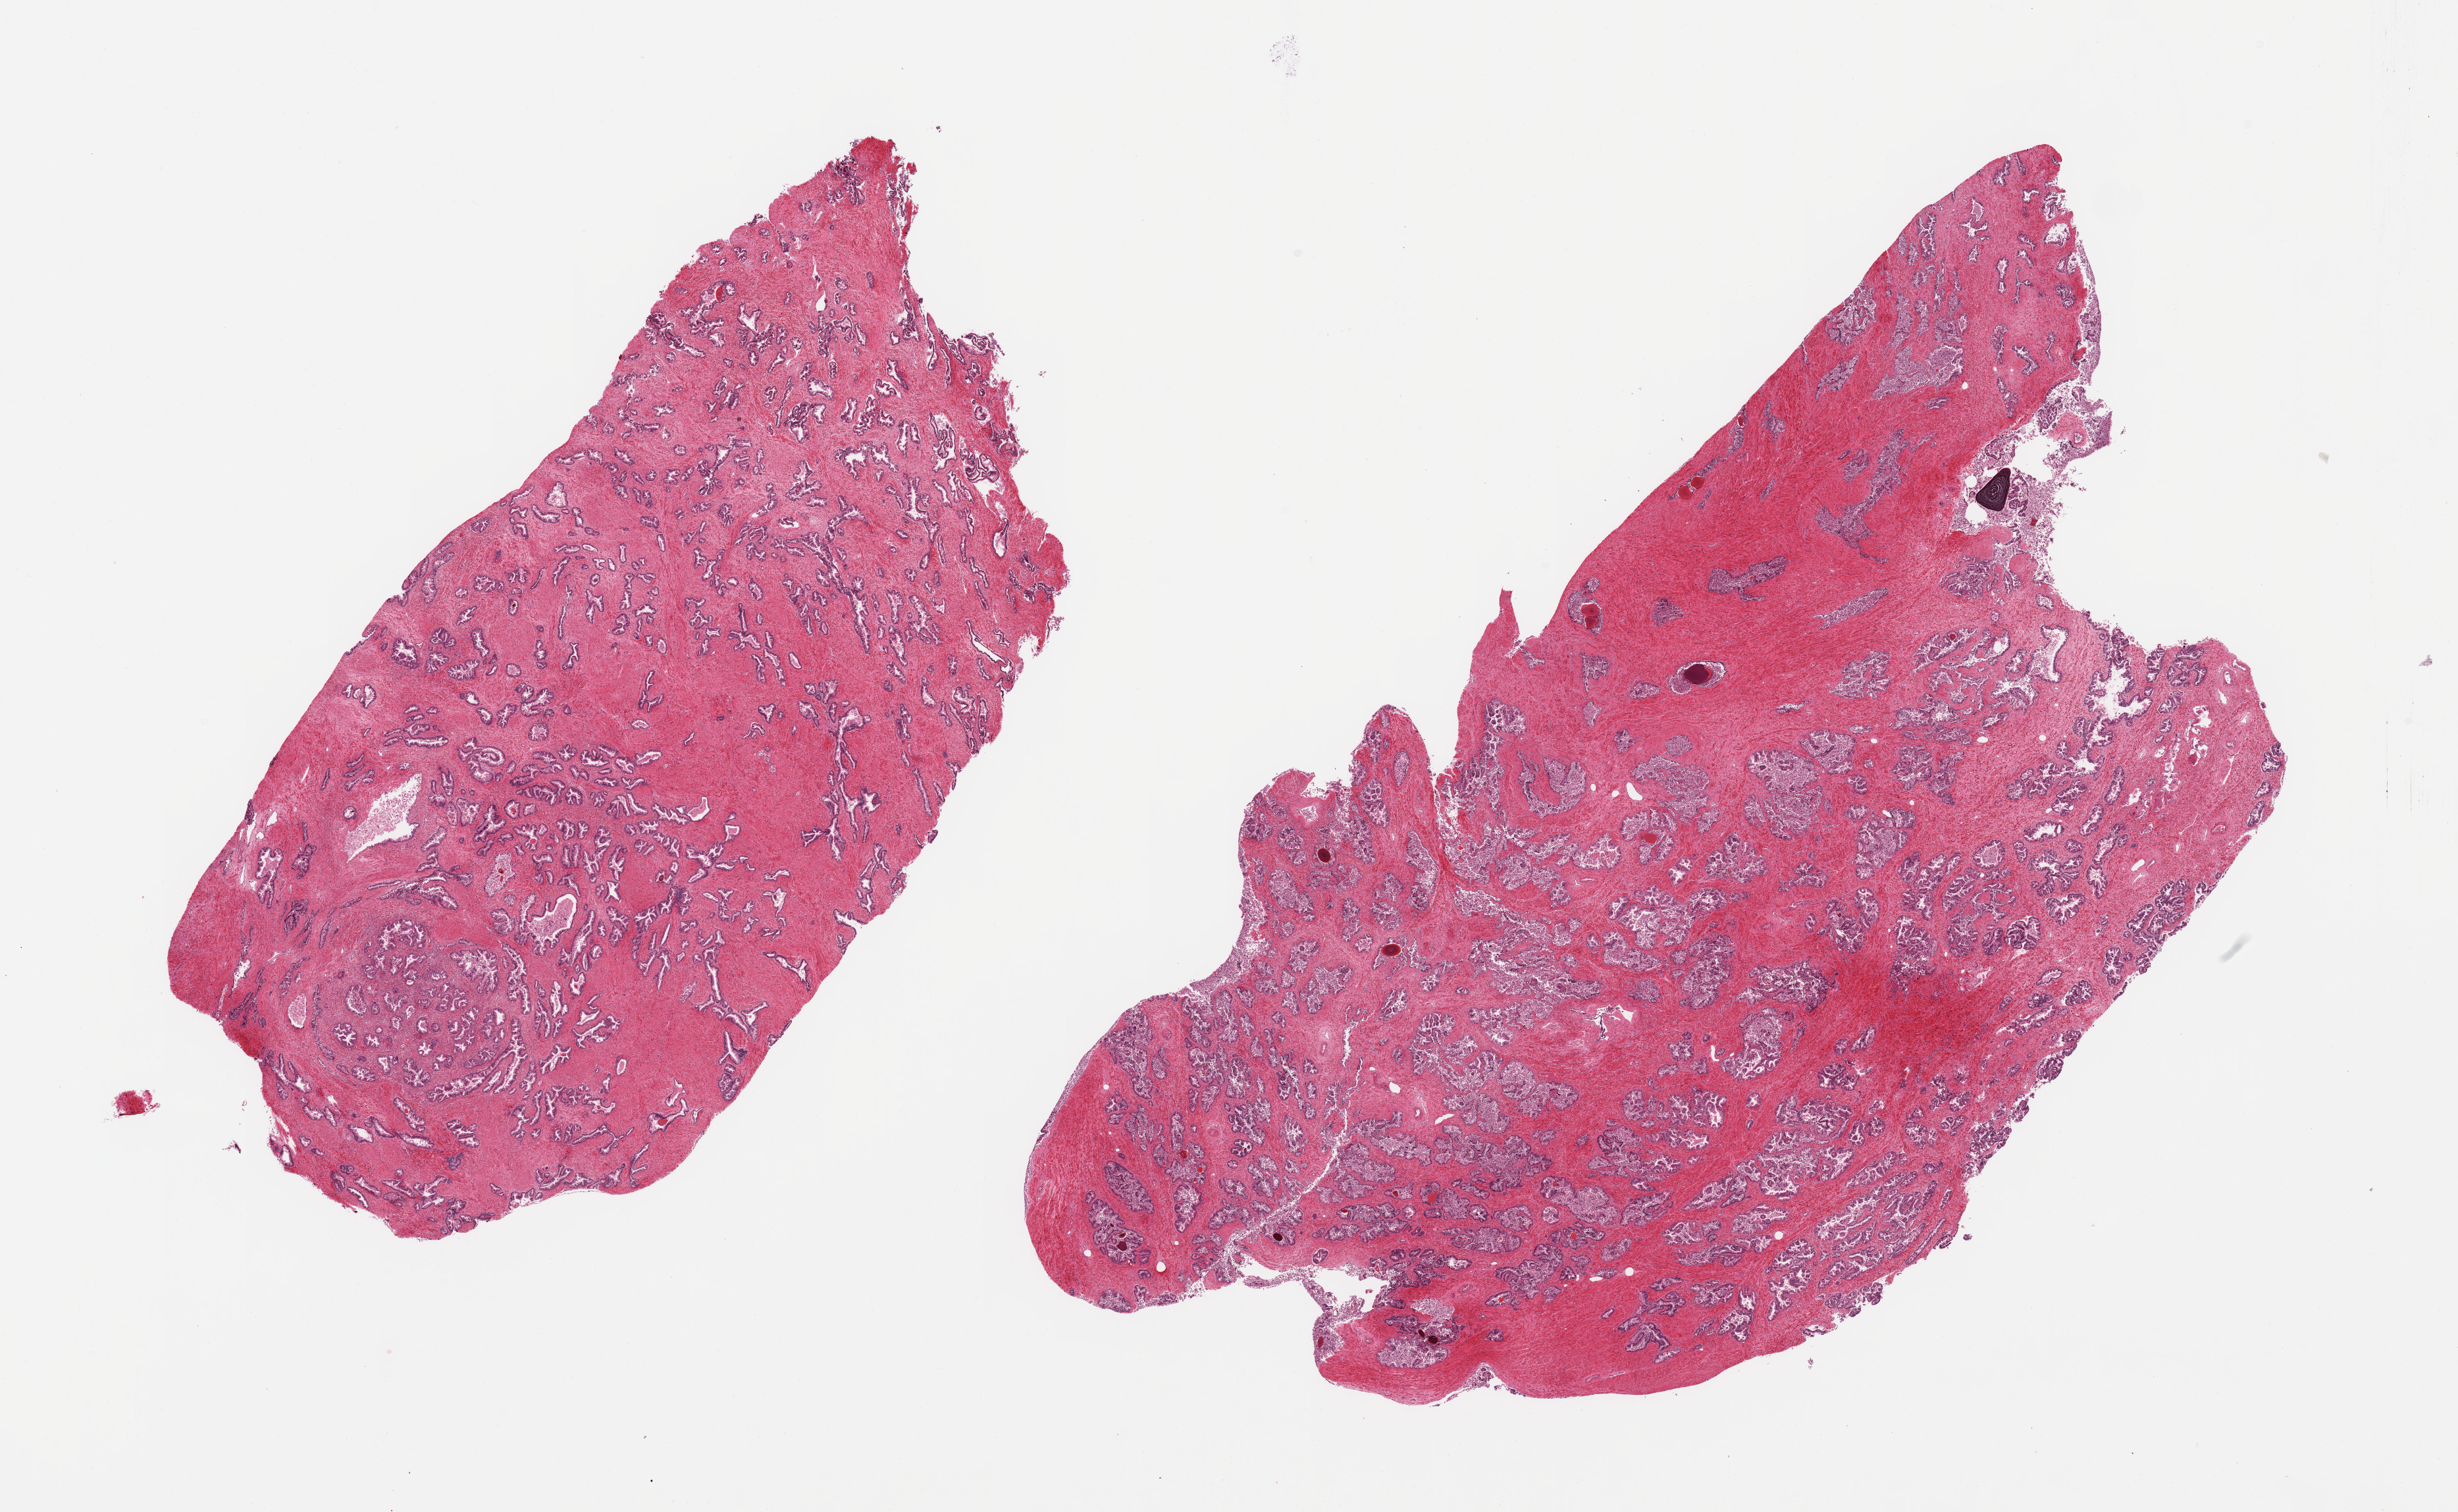
Haematoxylin and eosin whole-slide image — low-resolution overview of the scanned area, about 29.5 x 18.2 mm (from a 20x scan); PAXgene-fixed, paraffin-embedded tissue; section of prostate (target tissue); donor tissue sample. Donor sex: male.
Pathologist's review note for this sample: 2 pieces; some acini are severely autolyzed.